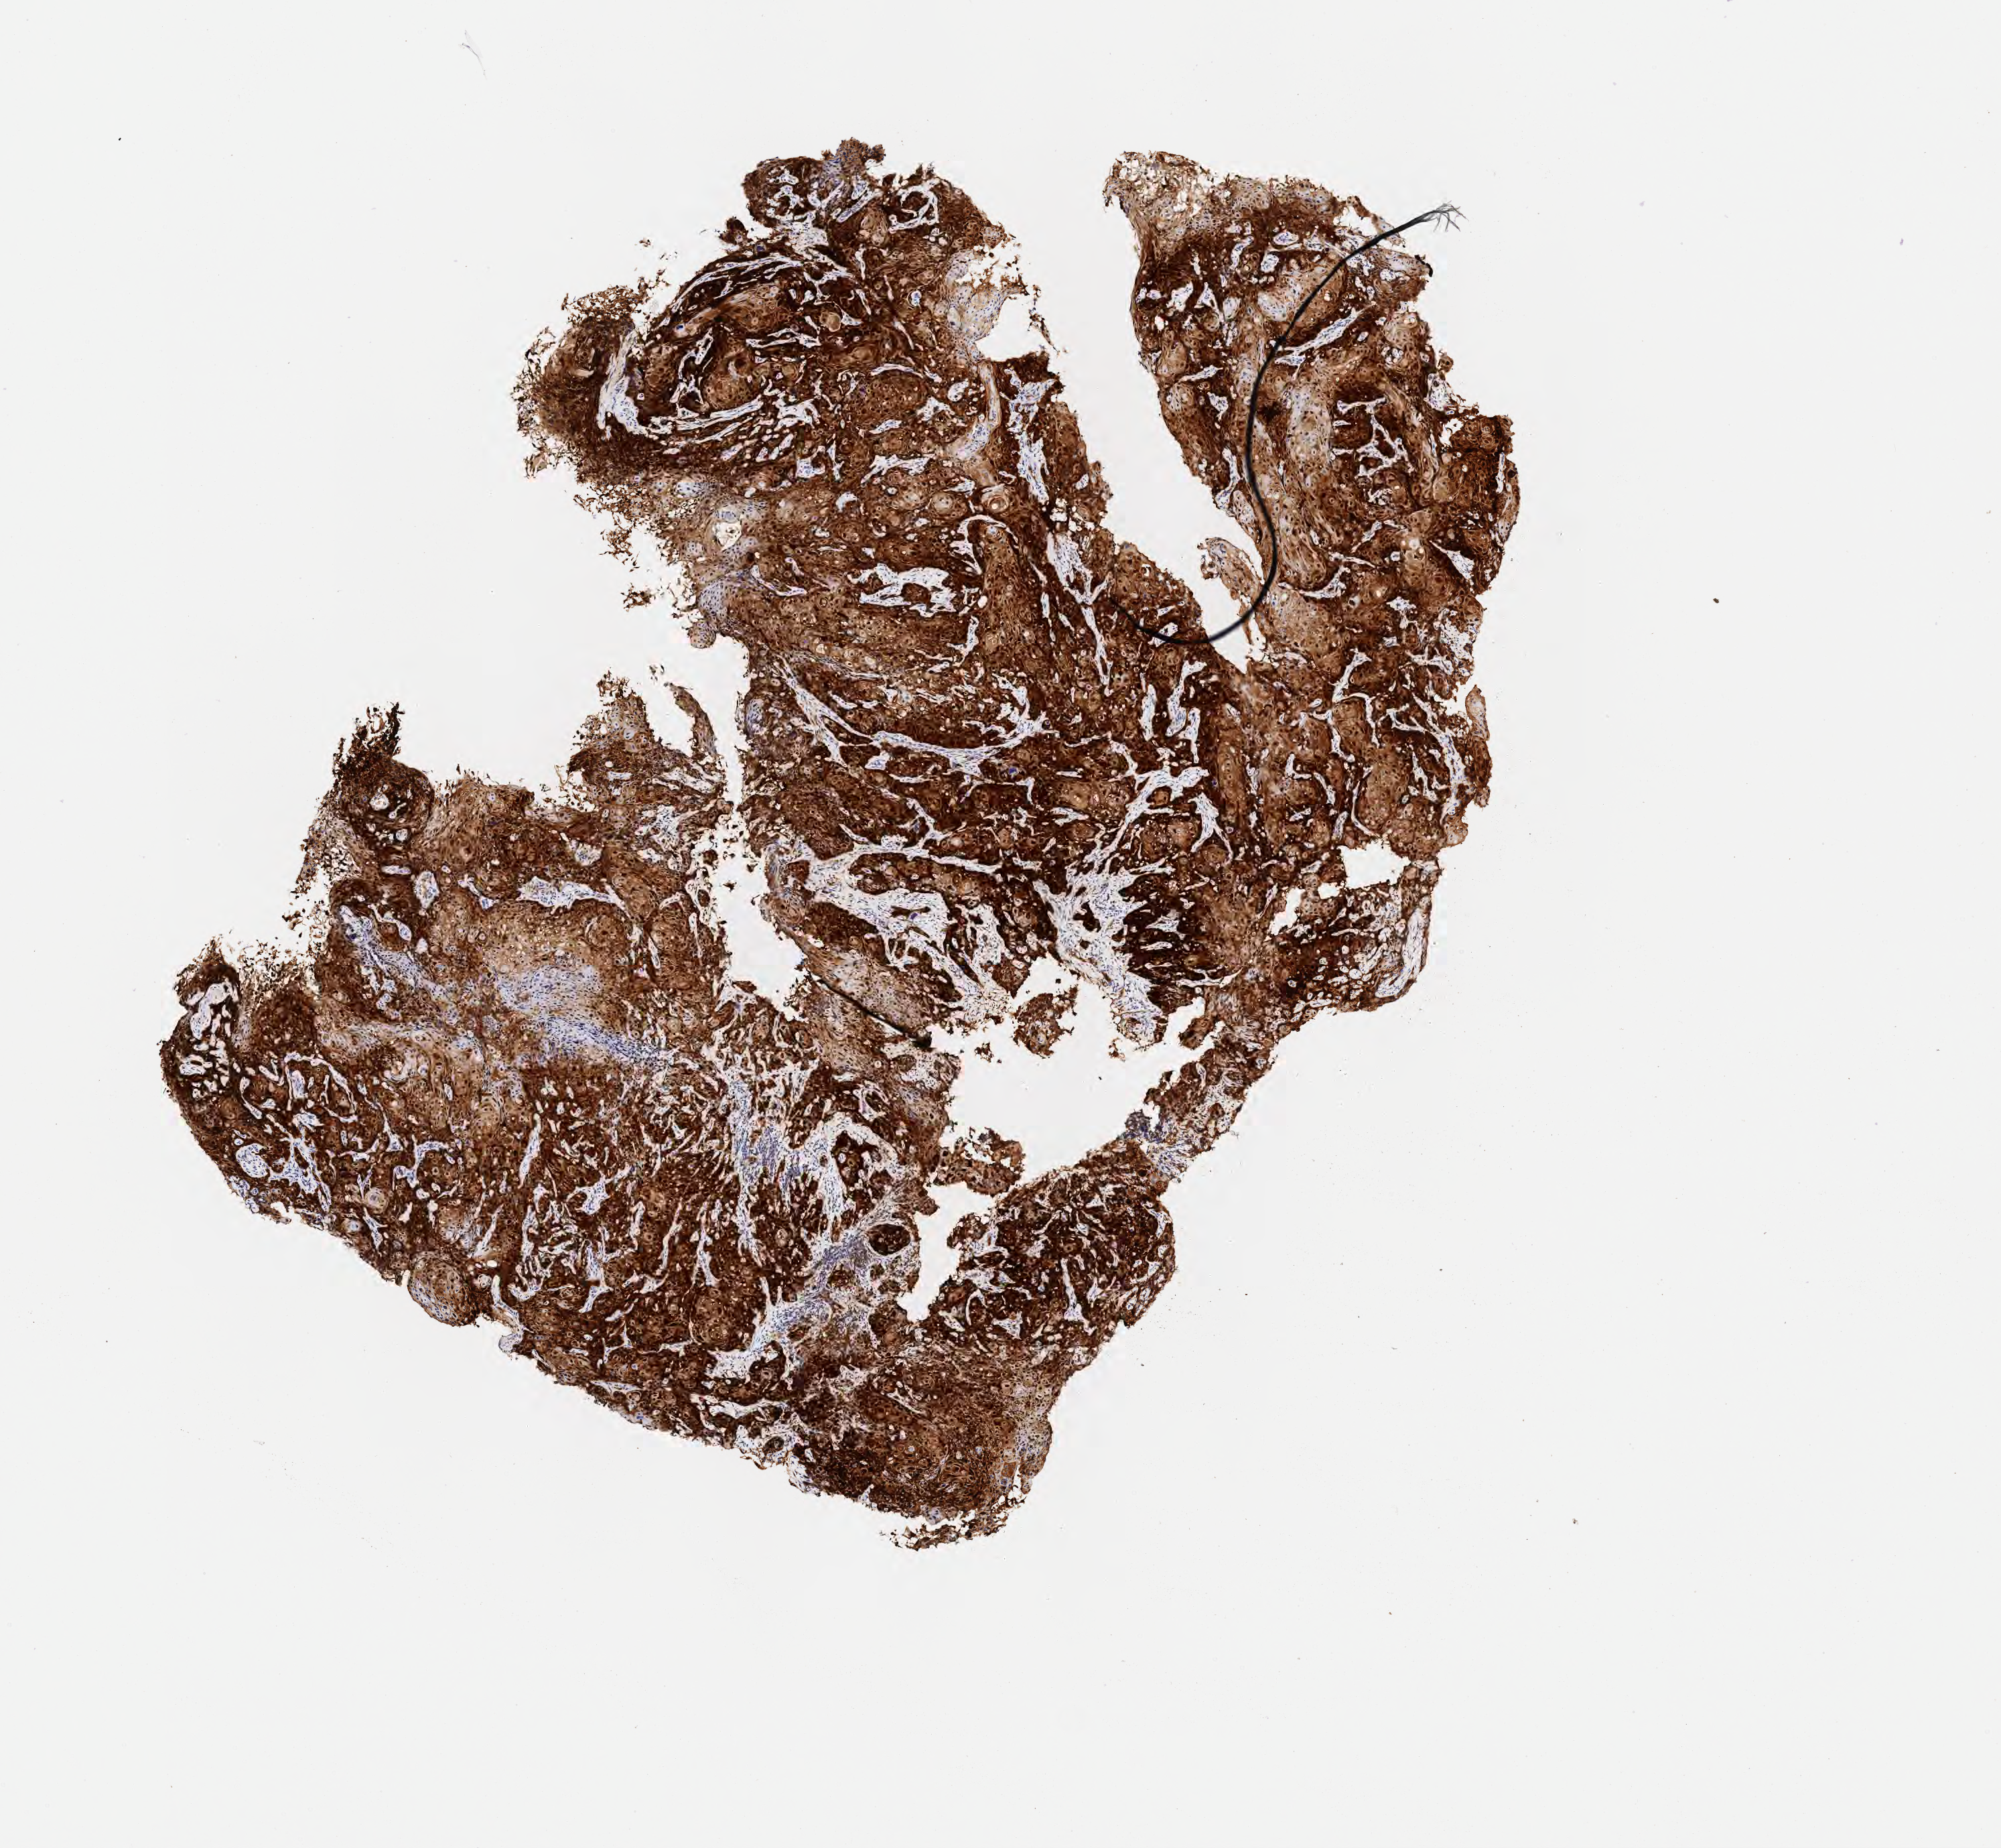
Immunohistochemistry (IHC) whole-slide image stained for p16 (p16INK4a) — whole scanned area (about 6.0 x 5.6 mm) shown as a low-resolution overview, specimen: tumor tissue, site: cervix. Patient female; aged 48.
Histologic diagnosis: Squamous cell carcinoma, keratinizing, NOS.